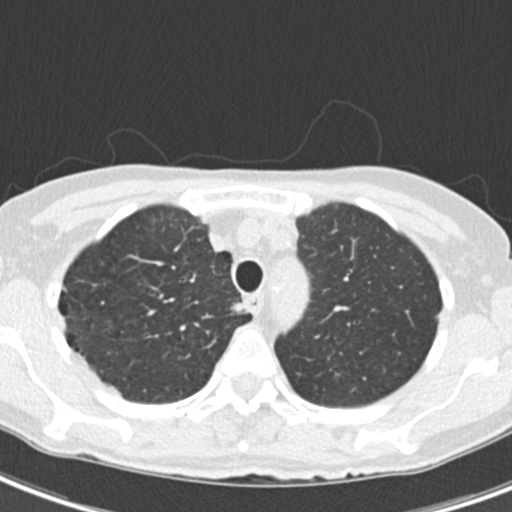
Chest CT (low-dose screening protocol), one axial image, second screening round (one year after baseline), lung window (W 1500 / L -600 HU), 2 mm slice thickness, standard (soft-tissue) reconstruction kernel (B30f), slice 43 of 218 in the series, 512 × 512 image matrix, field of view 286 × 286 mm. Female, age 68 years at enrolment. Current smoker at enrolment.
Expert-annotated lung lesion, bounding box [x1, y1, x2, y2] px = [229, 300, 253, 323]. No non-calcified nodule or mass ≥4 mm was recorded by the screening reader at this exam. Official screen result: negative screen, no significant abnormalities. Lung cancer was diagnosed 436 days after this screen: squamous cell carcinoma, NOS, right upper lobe, mediastinum, poorly differentiated (G3), stage IIIB (AJCC 6th edition), 43 mm at pathology.